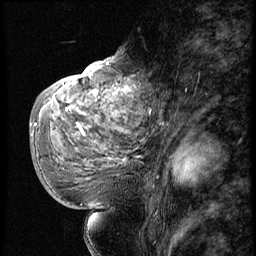
Breast MRI (dynamic contrast-enhanced), one sagittal slice; position 32 of 56 along the scan axis; 3 images stored at this slice position (order not interpretable as contrast timing); 1.5 T; TE 4.2 ms, TR 9 ms; 2.5 mm slice thickness; 256 × 256 image matrix. Patient: female, 51 years. Case-level facts recorded for this patient, not image findings: setting: breast cancer imaged before/during neoadjuvant chemotherapy; receptor status: triple-negative.
Annotated regions visible in this slice (semi-automatically segmented with operator editing):
- analysis volume of interest (the breast-tissue region the enhancement analysis was run in; not a lesion): bounding box (x1, y1, x2, y2) in pixels: (52, 66, 140, 179)
- tumour enhancement mask (voxels above the 140 % enhancement threshold inside the analysis volume of interest): (68, 66, 131, 135)